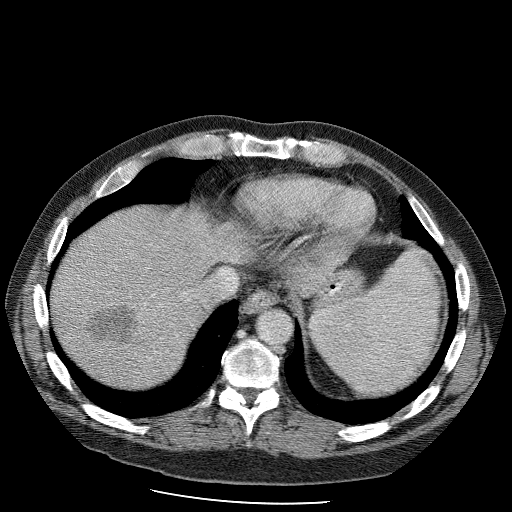
Contrast-enhanced abdominal CT (liver protocol), one axial slice; position 88 of 98 along the scan axis; 120 kVp; soft-tissue window (W 400 / L 40 HU); 2.5 mm slice thickness; 512 × 512 image matrix, field of view 400 × 400 mm. From the clinical record (not read from this slice): diagnosis: hepatocellular carcinoma (patient treated with transarterial chemoembolisation; whether this scan precedes or follows treatment is not stated here); TNM stage (as recorded): Stage-II; Child-Pugh class: B; tumour differentiation: moderately differentiated.
Outlined on this slice (semi-automatic segmentation, software-assisted and operator-edited):
- liver parenchyma outside the tumour (the mass and vessels are separate outlines, so this box may not span the whole liver): box from (x=52, y=208) to (x=232, y=382) px
- mass: (x=87, y=300)–(x=149, y=348)